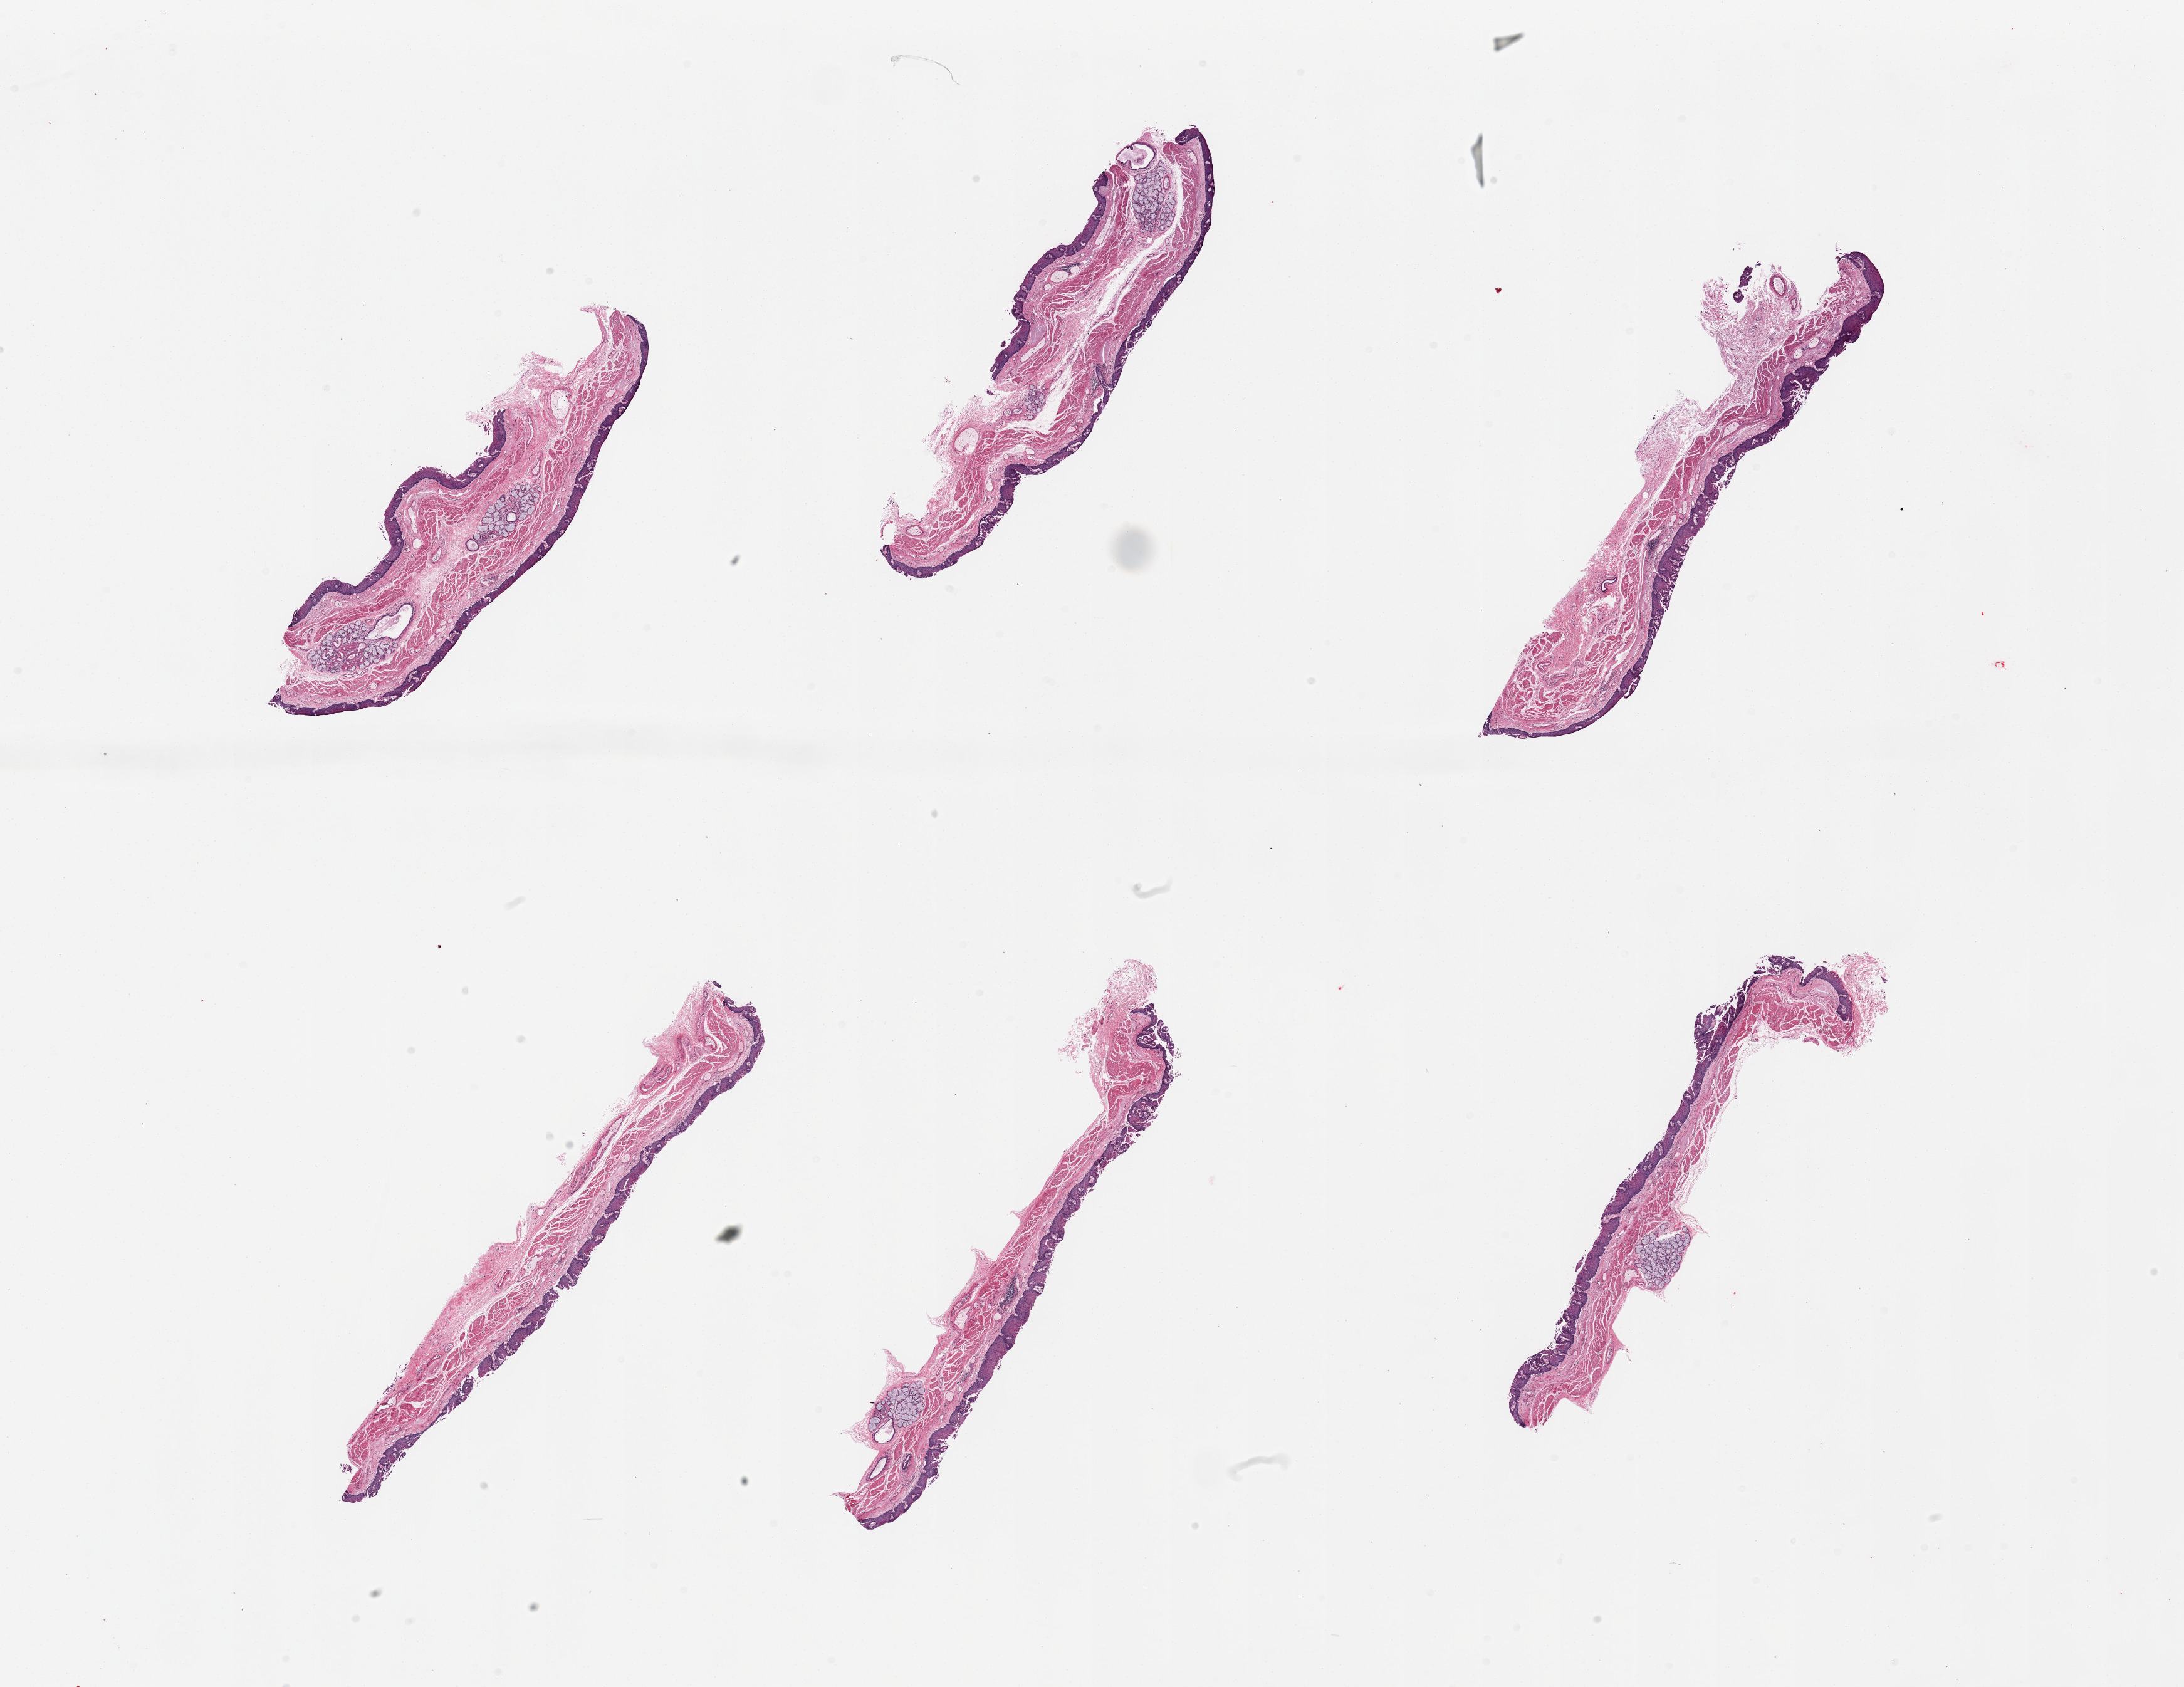
Digitized haematoxylin and eosin-stained section, brightfield — whole scanned area (about 27.6 x 21.3 mm, slide scanned at 20x) shown as a low-resolution overview. PAXgene-fixed paraffin-embedded (PFPE) section. Target tissue: esophageal mucous membrane. Tissue donor sample. Donor: male.
Review note (as recorded): 6 pieces, squamous mucosa ~120-150 microns, submucosal mucus glands present.